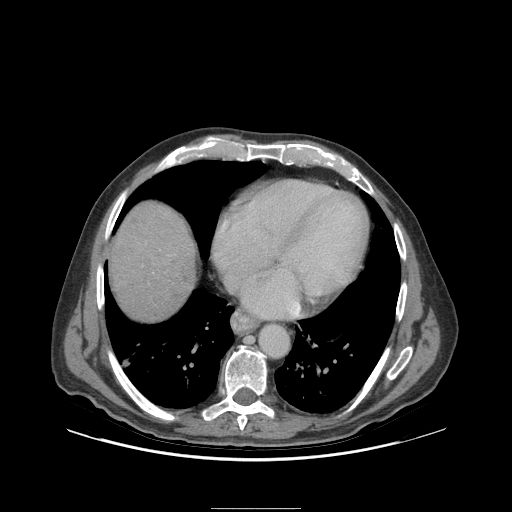
Contrast-enhanced abdominal CT (liver protocol), one axial slice; position 93 of 105 along the scan axis; reconstruction kernel STANDARD; 140 kVp; soft-tissue window (W 400 / L 40 HU); 2.5 mm slice thickness; 512 × 512 image matrix, field of view 440 × 440 mm. From the clinical record (not read from this slice): diagnosis: hepatocellular carcinoma (patient treated with transarterial chemoembolisation; whether this scan precedes or follows treatment is not stated here); TNM stage (as recorded): Stage-I; Child-Pugh class: A; tumour size: 5.1 cm.
Structures marked on this image (semi-automatically segmented with operator editing):
- liver parenchyma outside the tumour (the mass and vessels are separate outlines, so this box may not span the whole liver): bounding box [x1, y1, x2, y2] px = [108, 202, 196, 320]